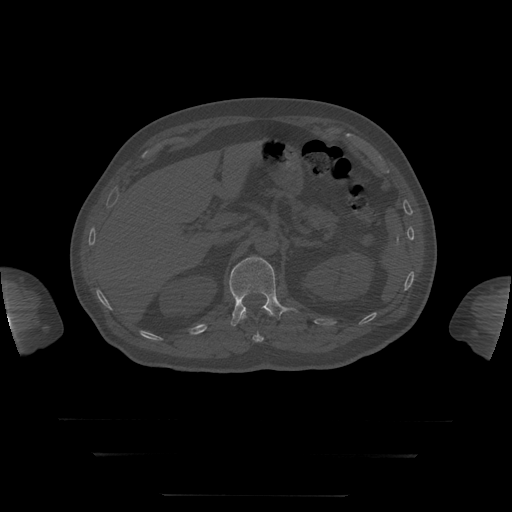
CT including the spine, one axial slice. Slice 57 of 397 in the series (ordered by position). Reconstruction kernel STANDARD. Bone window (W 1800 / L 400 HU). 1.25 mm slice thickness. 512 × 512 image matrix, field of view 510 × 510 mm. Patient age 73 years. Case-level facts recorded for this patient, not image findings: primary cancer: prostate.
Structures marked on this image (semi-automatic segmentation, software-assisted and operator-edited):
- L1 vertebra: bounding box <229,257,297,327> (left, top, right, bottom; pixels)
- T12 vertebra: <240,313,264,342>
- T8 vertebra: <241,299,273,316>